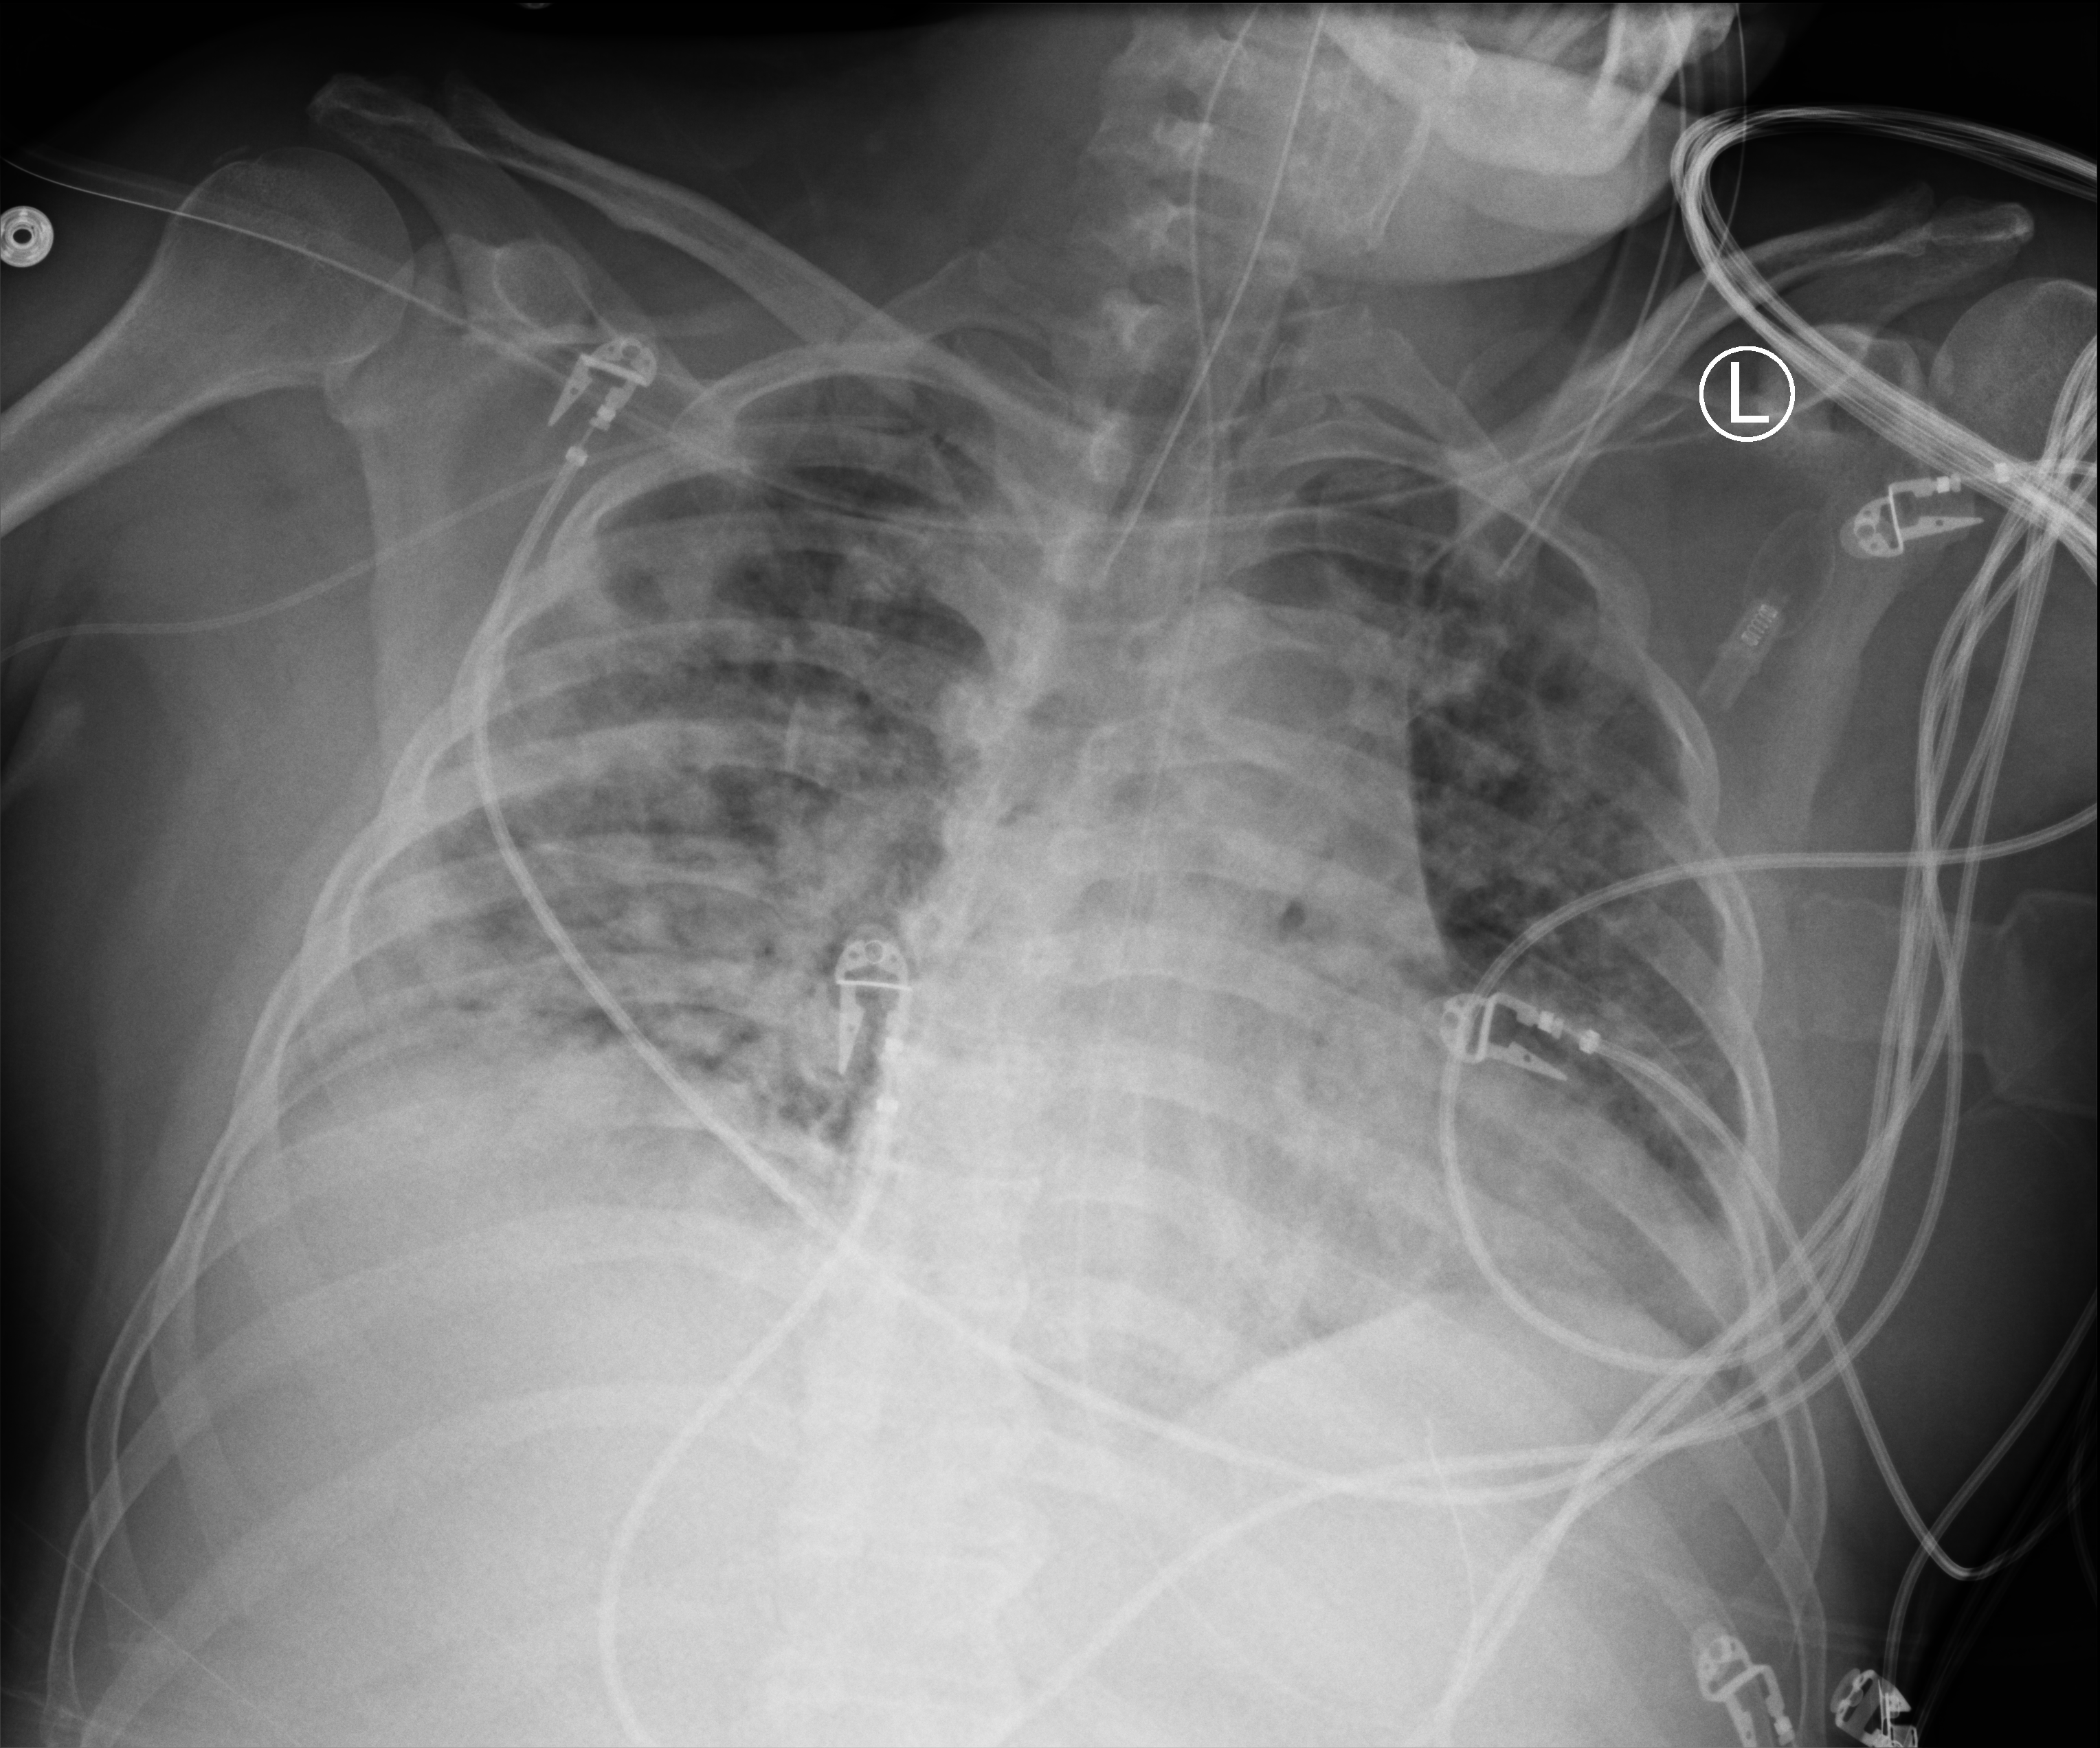
Chest X-ray (portable); anteroposterior (AP) projection. Male patient hospitalised with COVID-19, age 18–59 years.
From the hospital-stay record, not from the radiograph (when in the stay this image was taken is not recorded): admitted to intensive care during this hospital stay: yes.